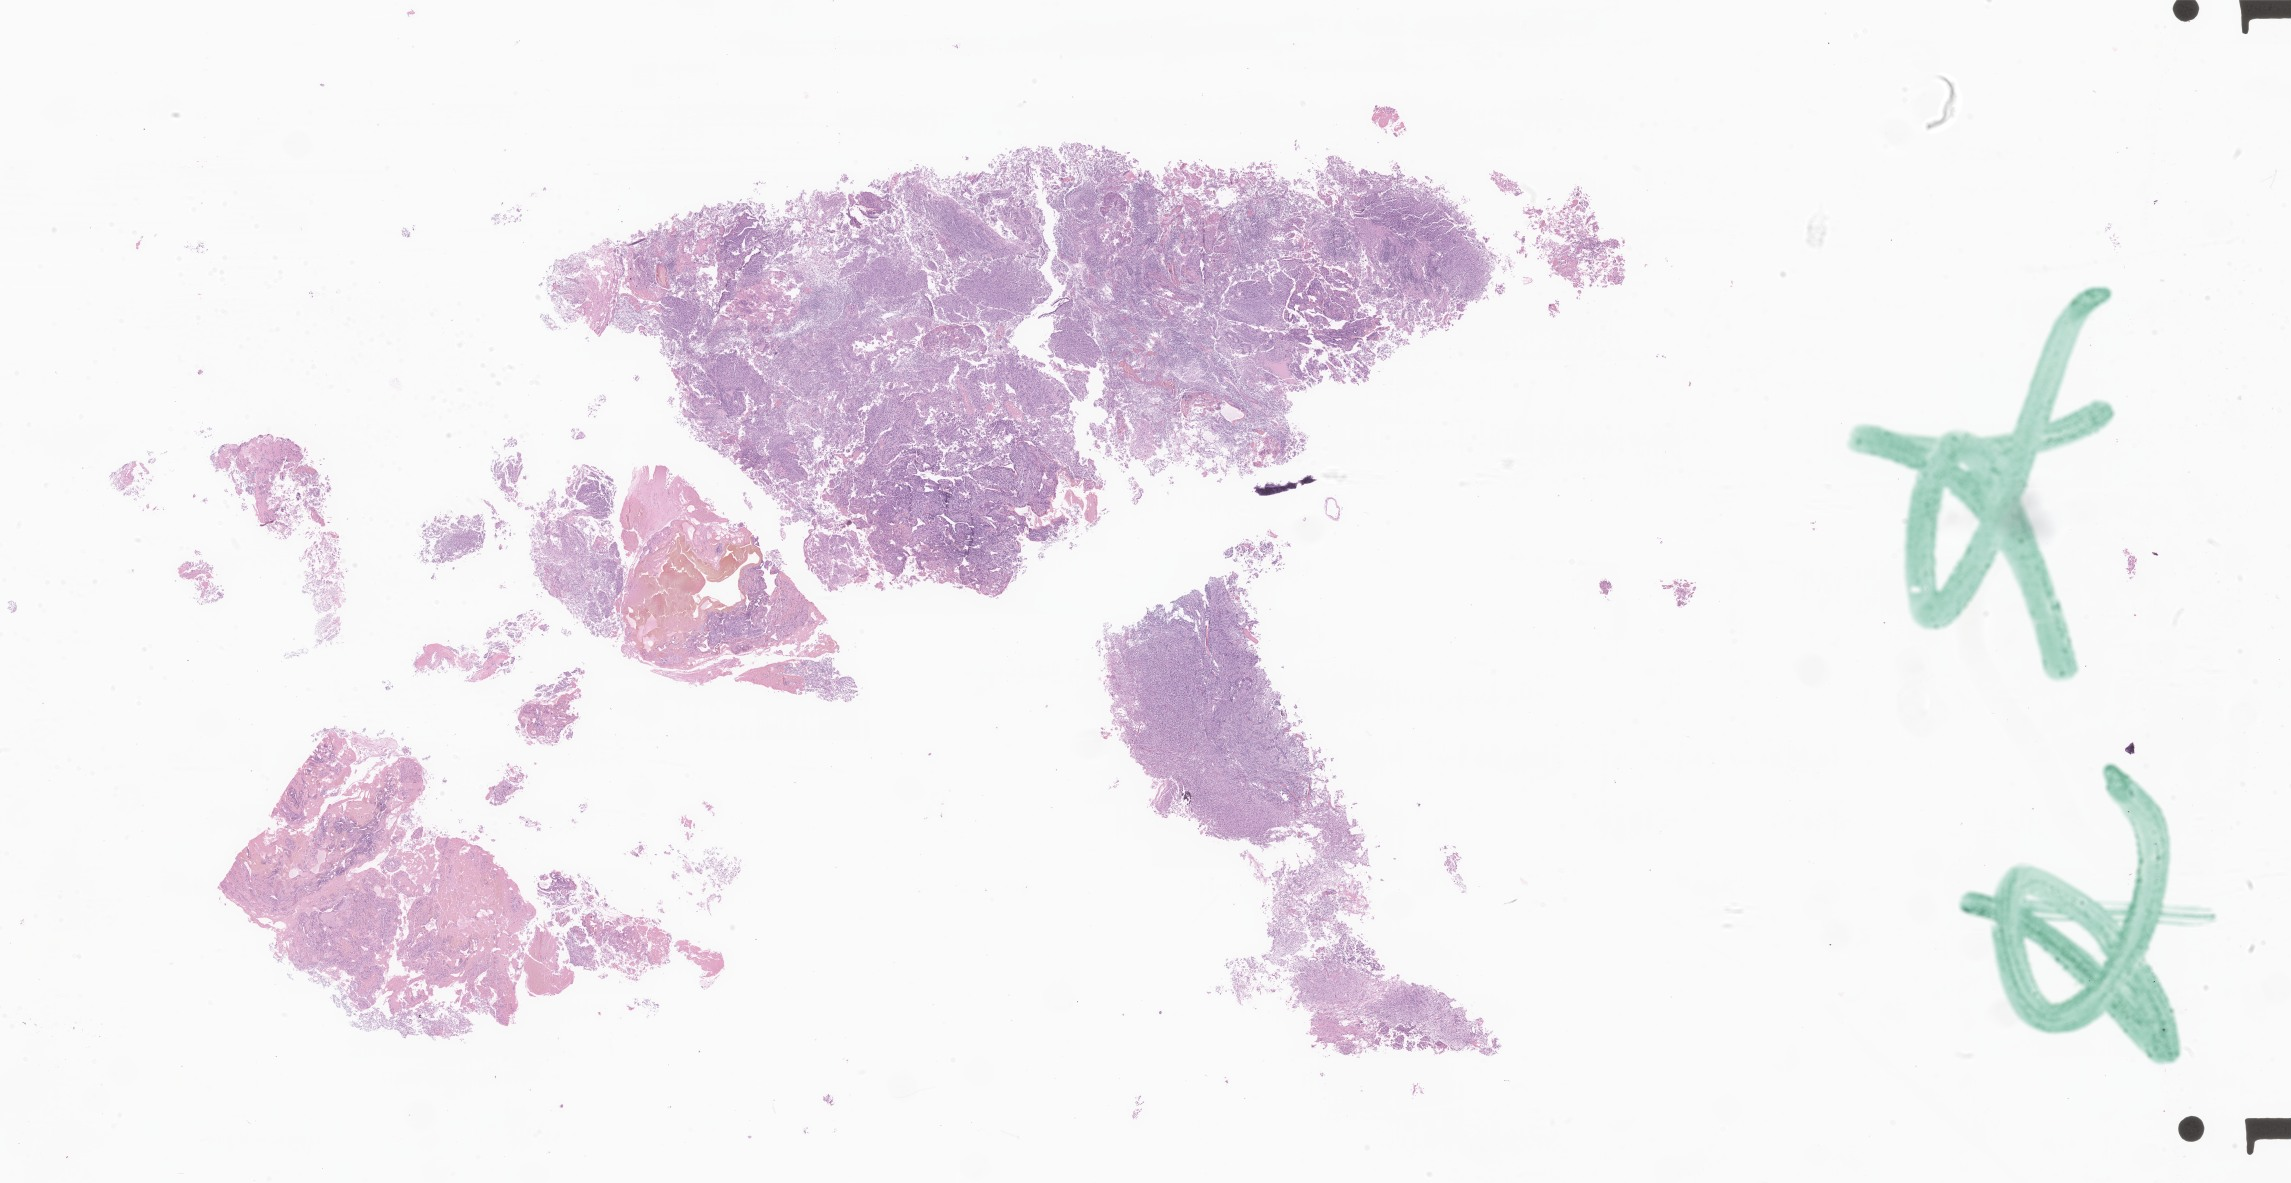
Whole-slide image, H&E stain of tumor tissue from the brain, shown as a low-resolution overview of the whole scanned area (about 38.6 x 20.0 mm), formalin-fixed, paraffin-embedded (FFPE) tissue. Patient female; age 80 months (6 years 8 months).
Diagnosis (ICD-O-3 morphology term): CNS embryonal tumor, NOS.